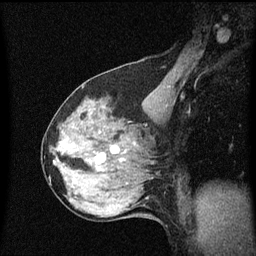
Breast MRI (dynamic contrast-enhanced), one sagittal slice; dynamic contrast-enhanced series, image 2 of 3 at this slice position (ordered by acquisition); 1.5 T; TE 4.2 ms, TR 8.4 ms; 2 mm slice thickness; 256 × 256 image matrix, field of view 200 × 200 mm. Female patient, age 64 years. Case-level facts recorded for this patient, not image findings: setting: breast cancer imaged before/during neoadjuvant chemotherapy; receptor status: HR-positive, HER2-negative.
Outlined on this slice (semi-automatic segmentation, software-assisted and operator-edited):
- analysis volume of interest (the breast-tissue region the enhancement analysis was run in; not a lesion): bounding box <56,92,142,175> (left, top, right, bottom; pixels)
- tumour enhancement mask (voxels above the 70 % enhancement threshold inside the analysis volume of interest): <97,160,100,165>